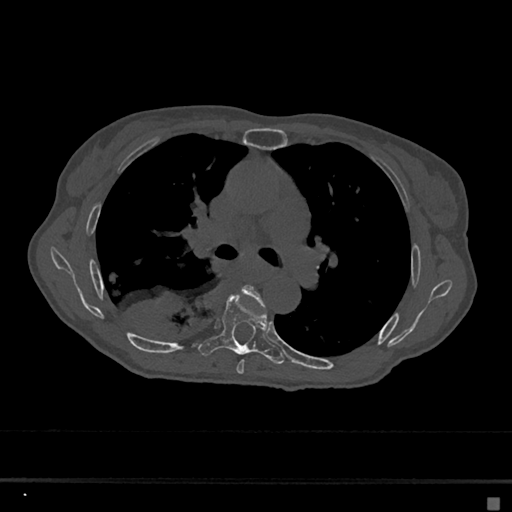
CT including the spine, one axial slice. Position 430 of 797 along the scan axis. Reconstruction kernel Br40s/3. Bone window (W 1800 / L 400 HU). 0.5 mm slice thickness. 512 × 512 image matrix, field of view 360 × 360 mm. Patient: female, 68 years. From the clinical record (not read from this slice): primary cancer: renal.
Outlined on this slice (semi-automatically segmented with operator editing):
- T5 vertebra: bounding box [x1, y1, x2, y2] px = [236, 285, 266, 375]
- T6 vertebra: [199, 291, 284, 364]